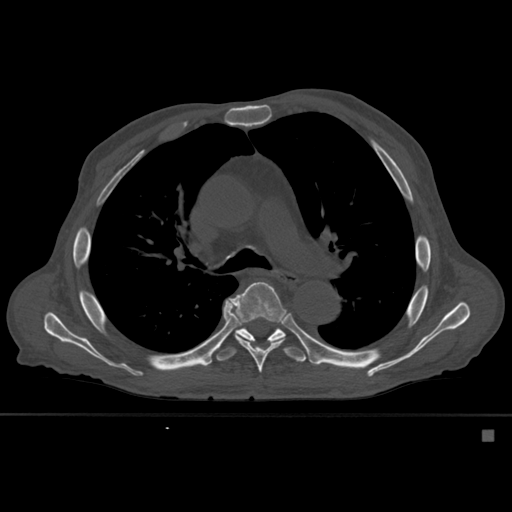
CT including the spine, one axial slice; slice 379 of 527 in the series (ordered by position); bone window (W 1800 / L 400 HU); 1.5 mm slice thickness; 512 × 512 image matrix, field of view 373 × 373 mm. Patient: male, 78 years. From the clinical record (not read from this slice): primary cancer: prostate.
Outlined on this slice (semi-automatically segmented with operator editing):
- T6 vertebra: box from (x=225, y=281) to (x=288, y=373) px
- T7 vertebra: (x=213, y=327)–(x=307, y=362)